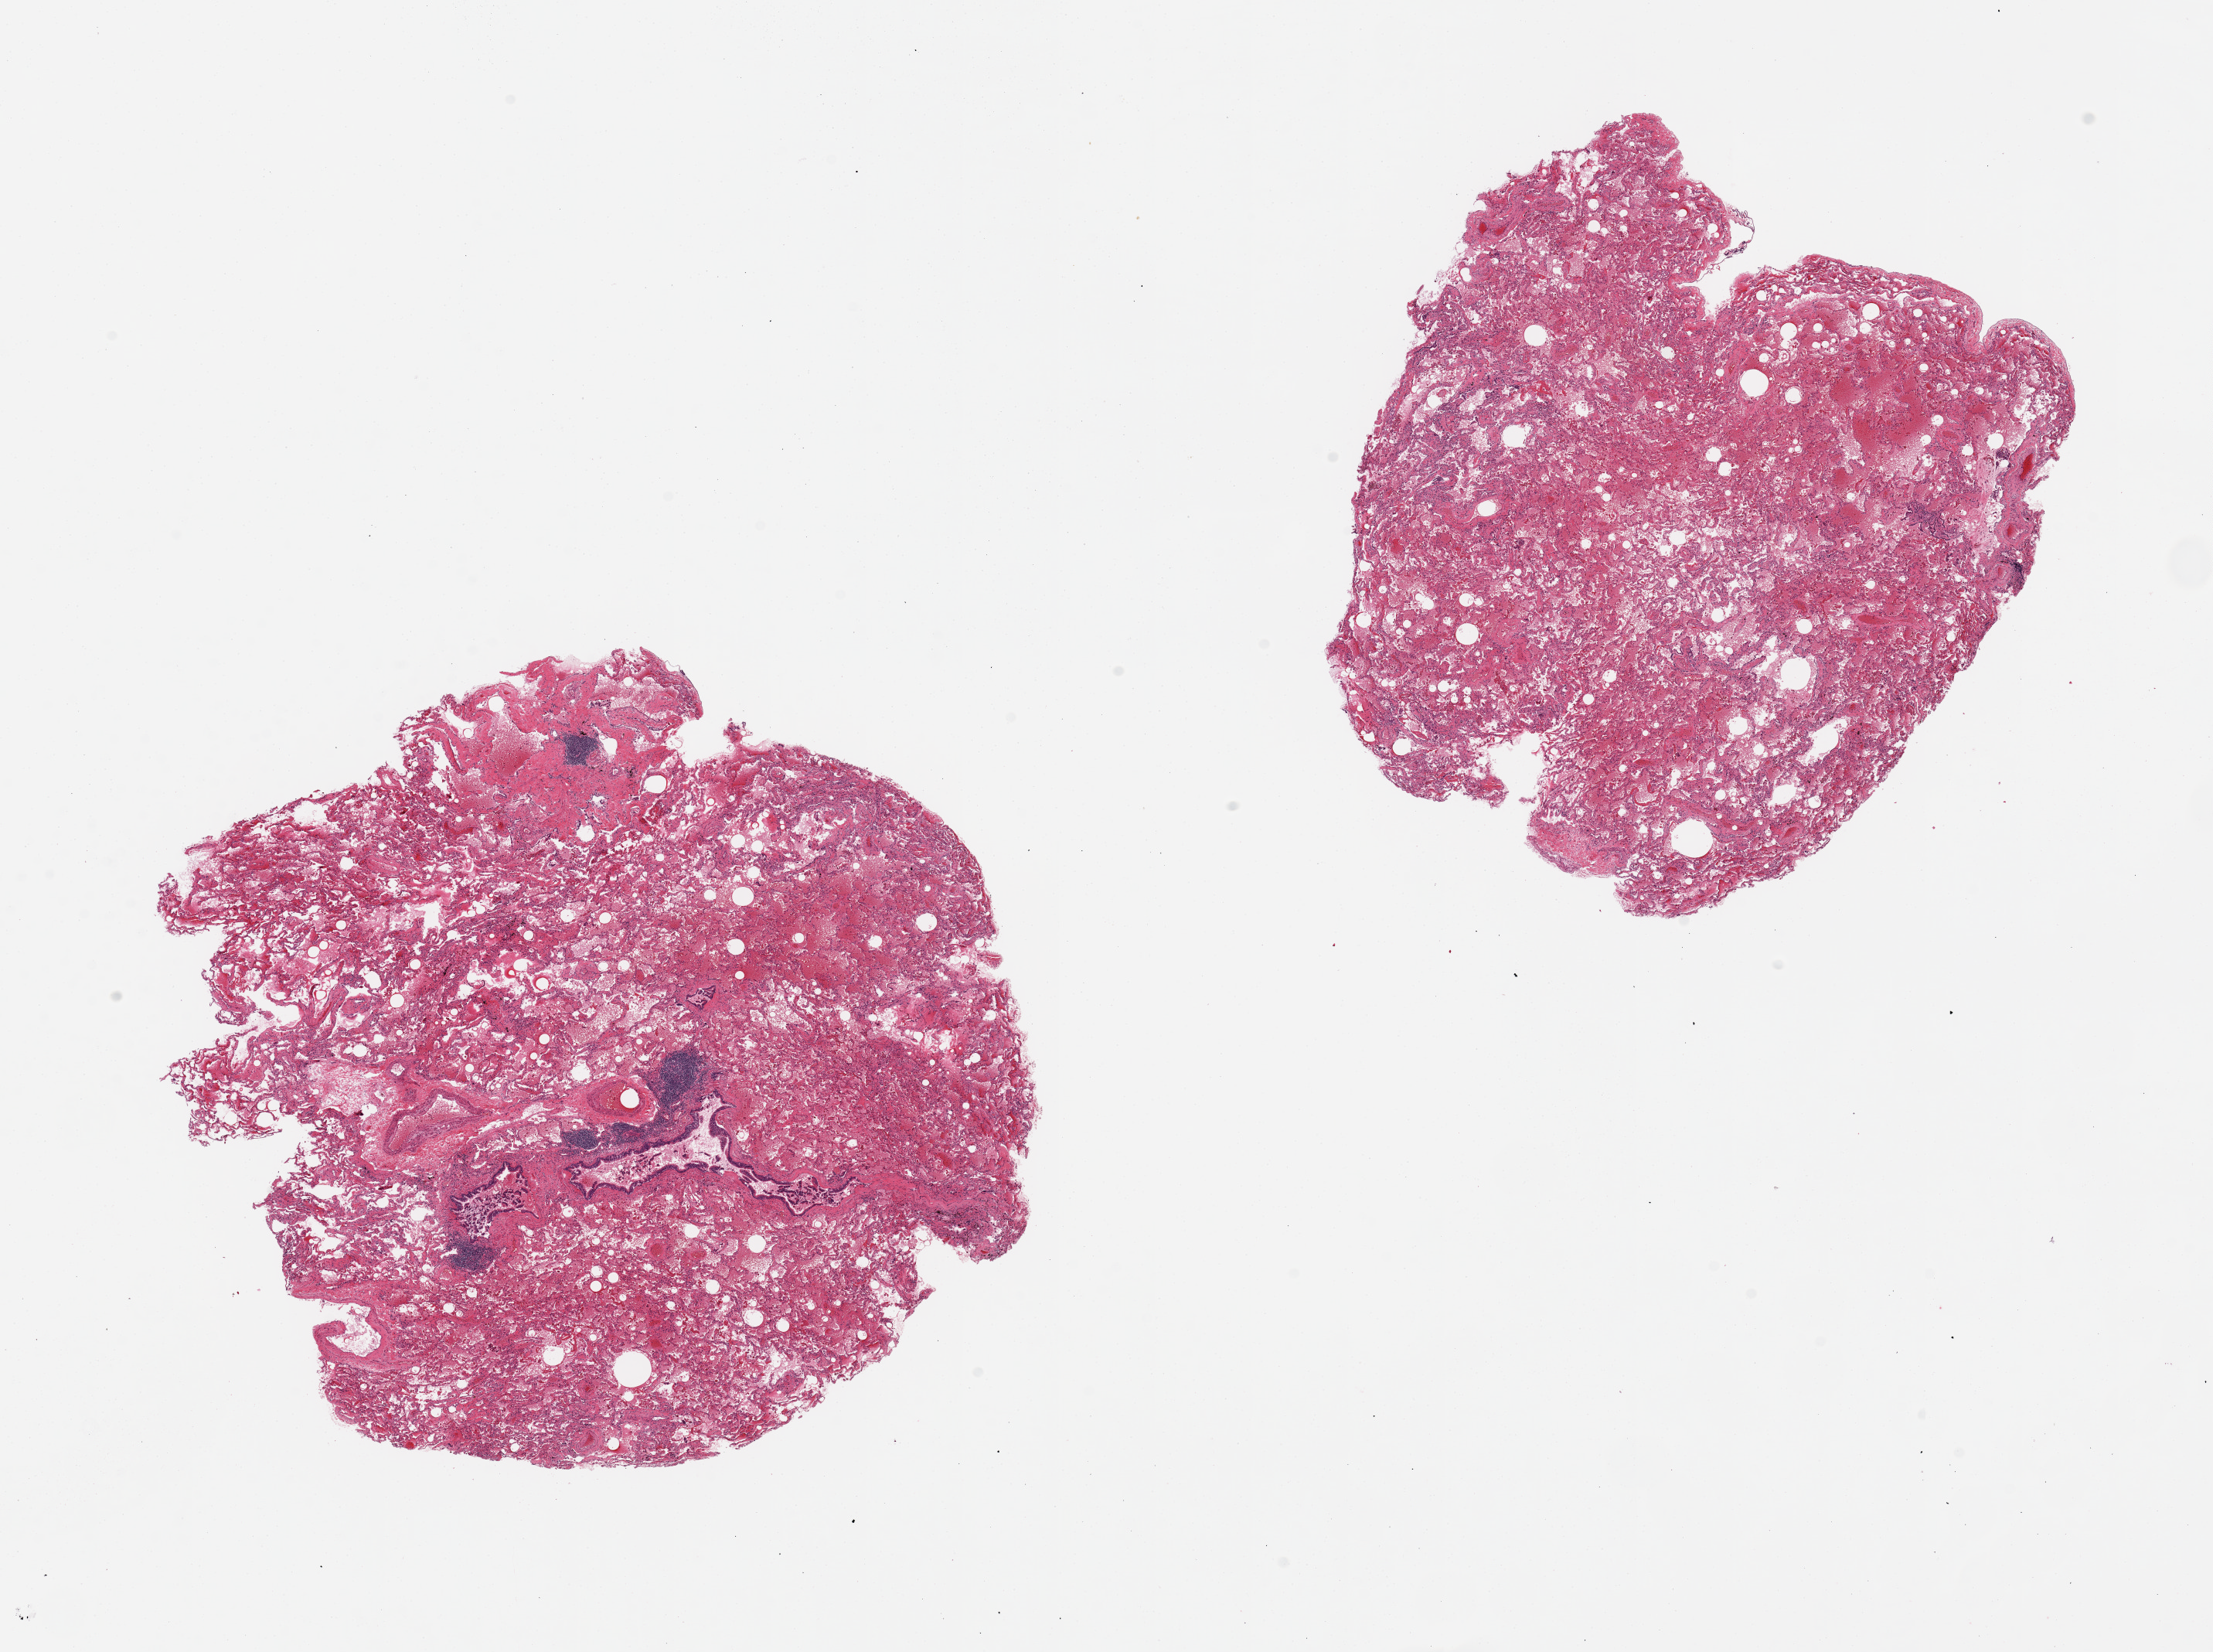
H&E whole-slide image, low-resolution overview of the scanned area, about 22.6 x 16.9 mm. PAXgene-fixed paraffin-embedded (PFPE) section. Target tissue: lung. Tissue donor sample. Female donor.
Pathologist's review note for this sample: 2 pieces, 9x8.5 & 7x7mm; extensive alveolar hemorrhage, some hyalin membranes, moderate interstitial fibrosis.